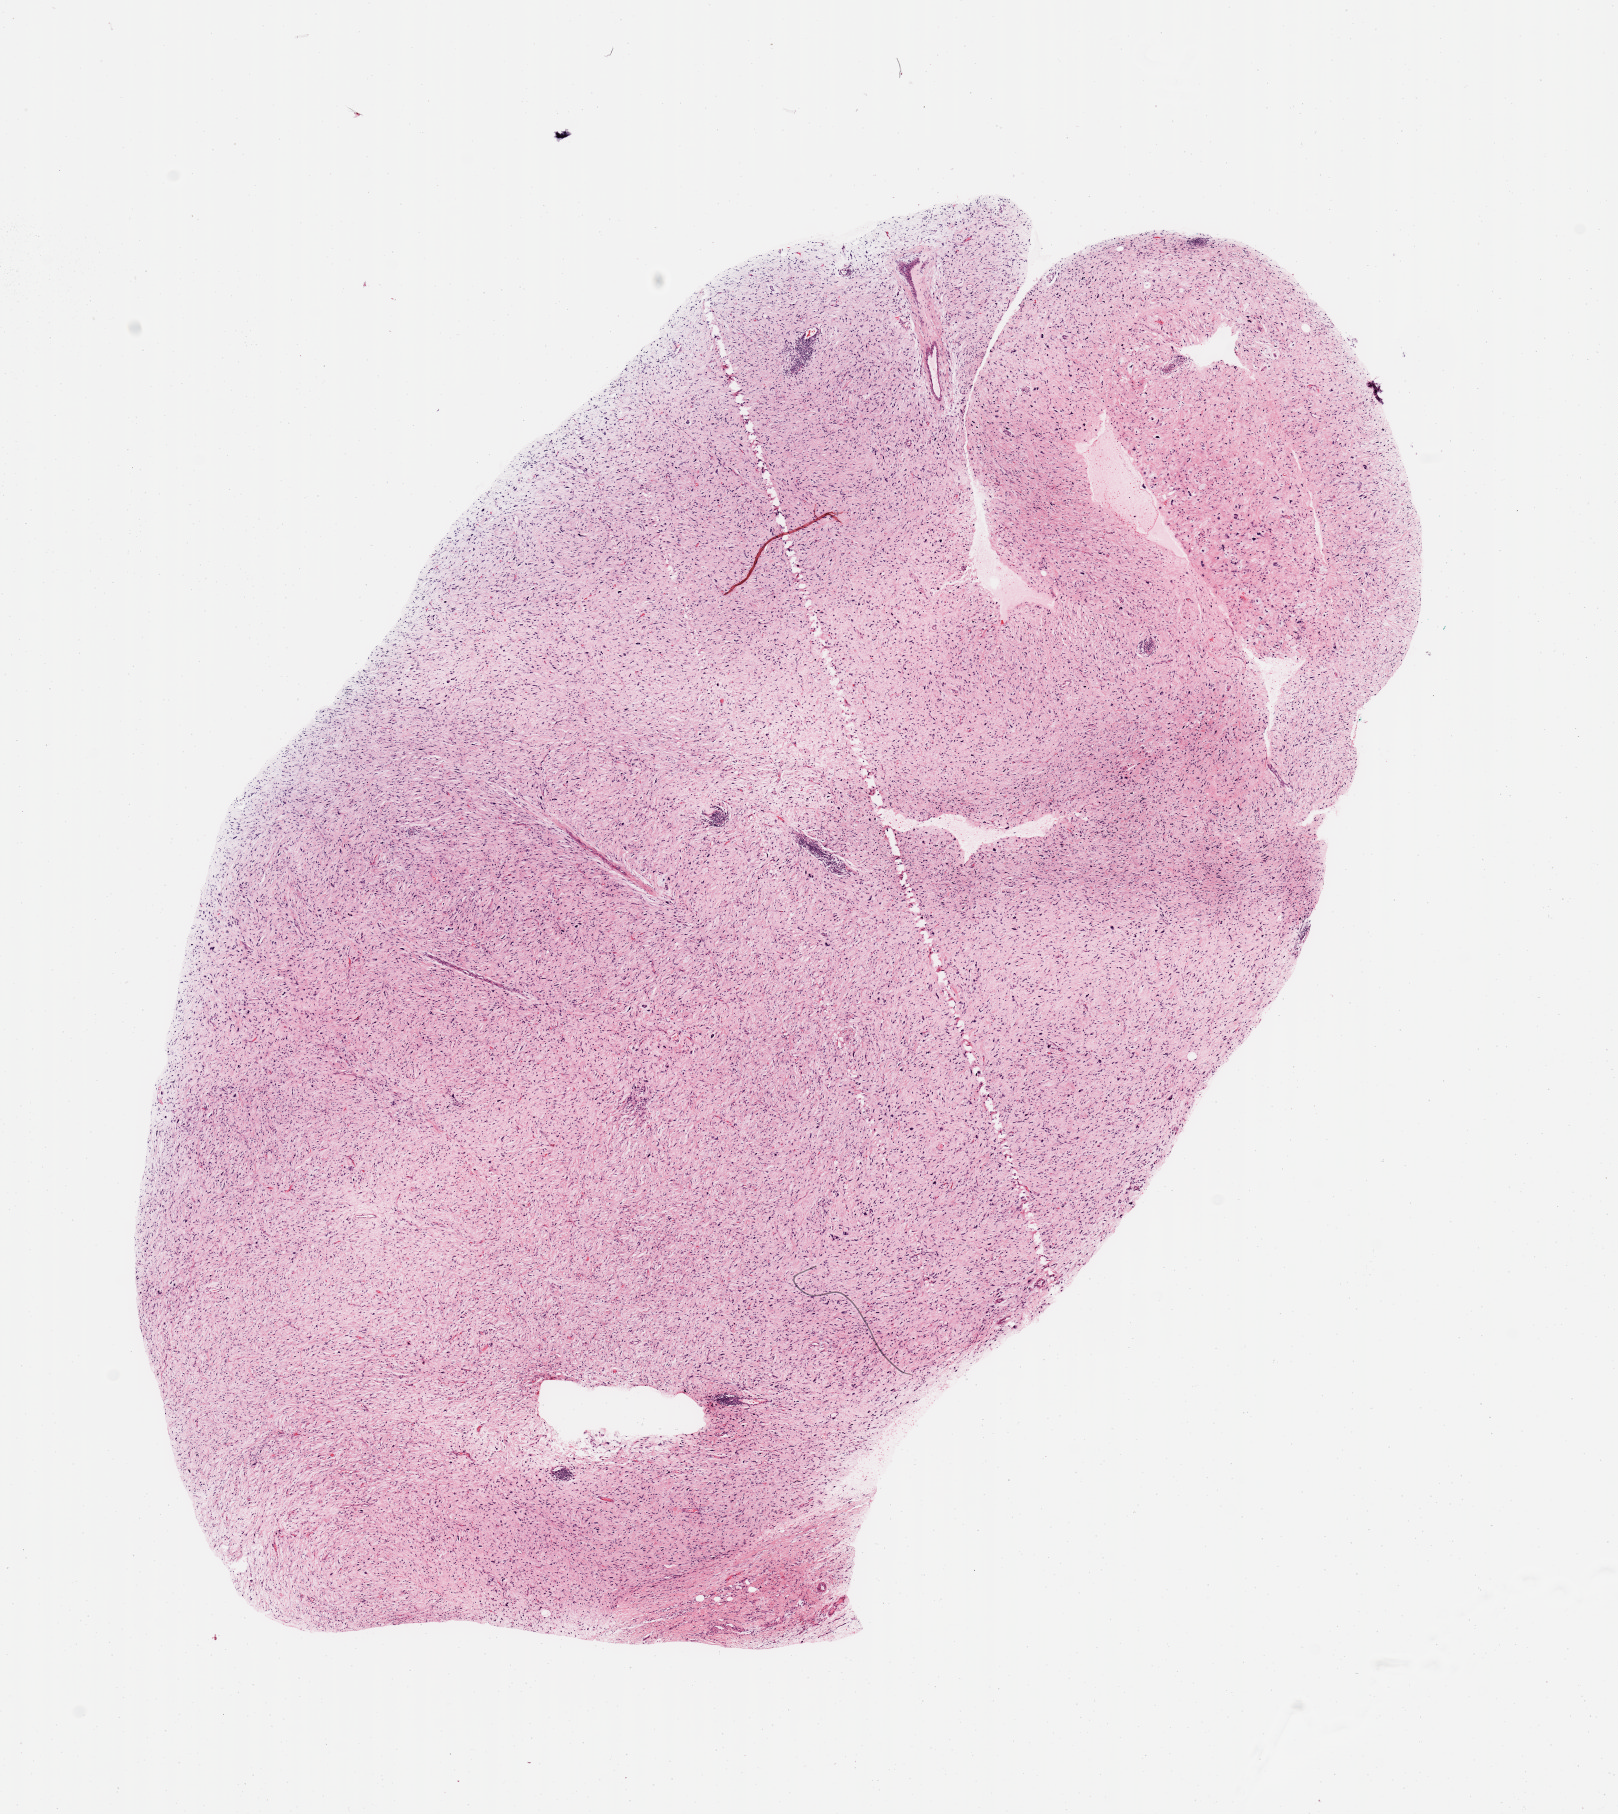
Whole-slide histology image, H&E — a low-resolution overview of the entire scanned area, about 12.8 x 14.3 mm (acquisition: 20x scan); tumour tissue sample. Female, 54 y/o.
• primary tumour site (as recorded): retroperitoneum
• patient diagnosis (cohort enrolment): sarcoma (site not recorded at cohort level)